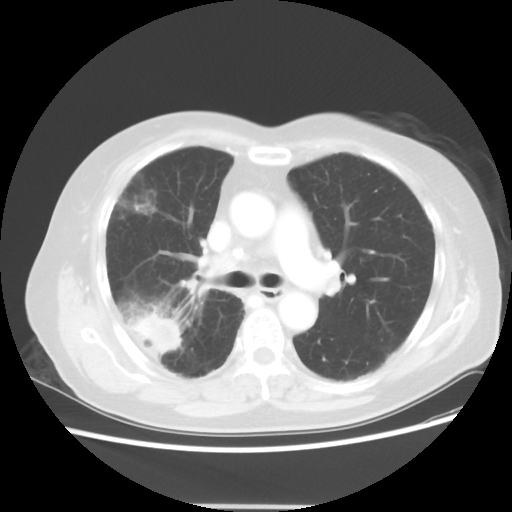
Chest CT, one axial slice. Position 30 of 50 along the scan axis. Reconstruction kernel STANDARD. Lung window (W 1500 / L -600 HU). 5 mm slice thickness. 512 × 512 image matrix, field of view 360 × 360 mm. Patient: female, 72 years. From the clinical record (not read from this slice): clinical TNM (as recorded): T2 N1 M0.
Annotated regions visible in this slice (bounding box drawn by a radiologist):
- lung tumour (recorded histology: adenocarcinoma): bounding box [x1, y1, x2, y2] px = [130, 311, 181, 355]